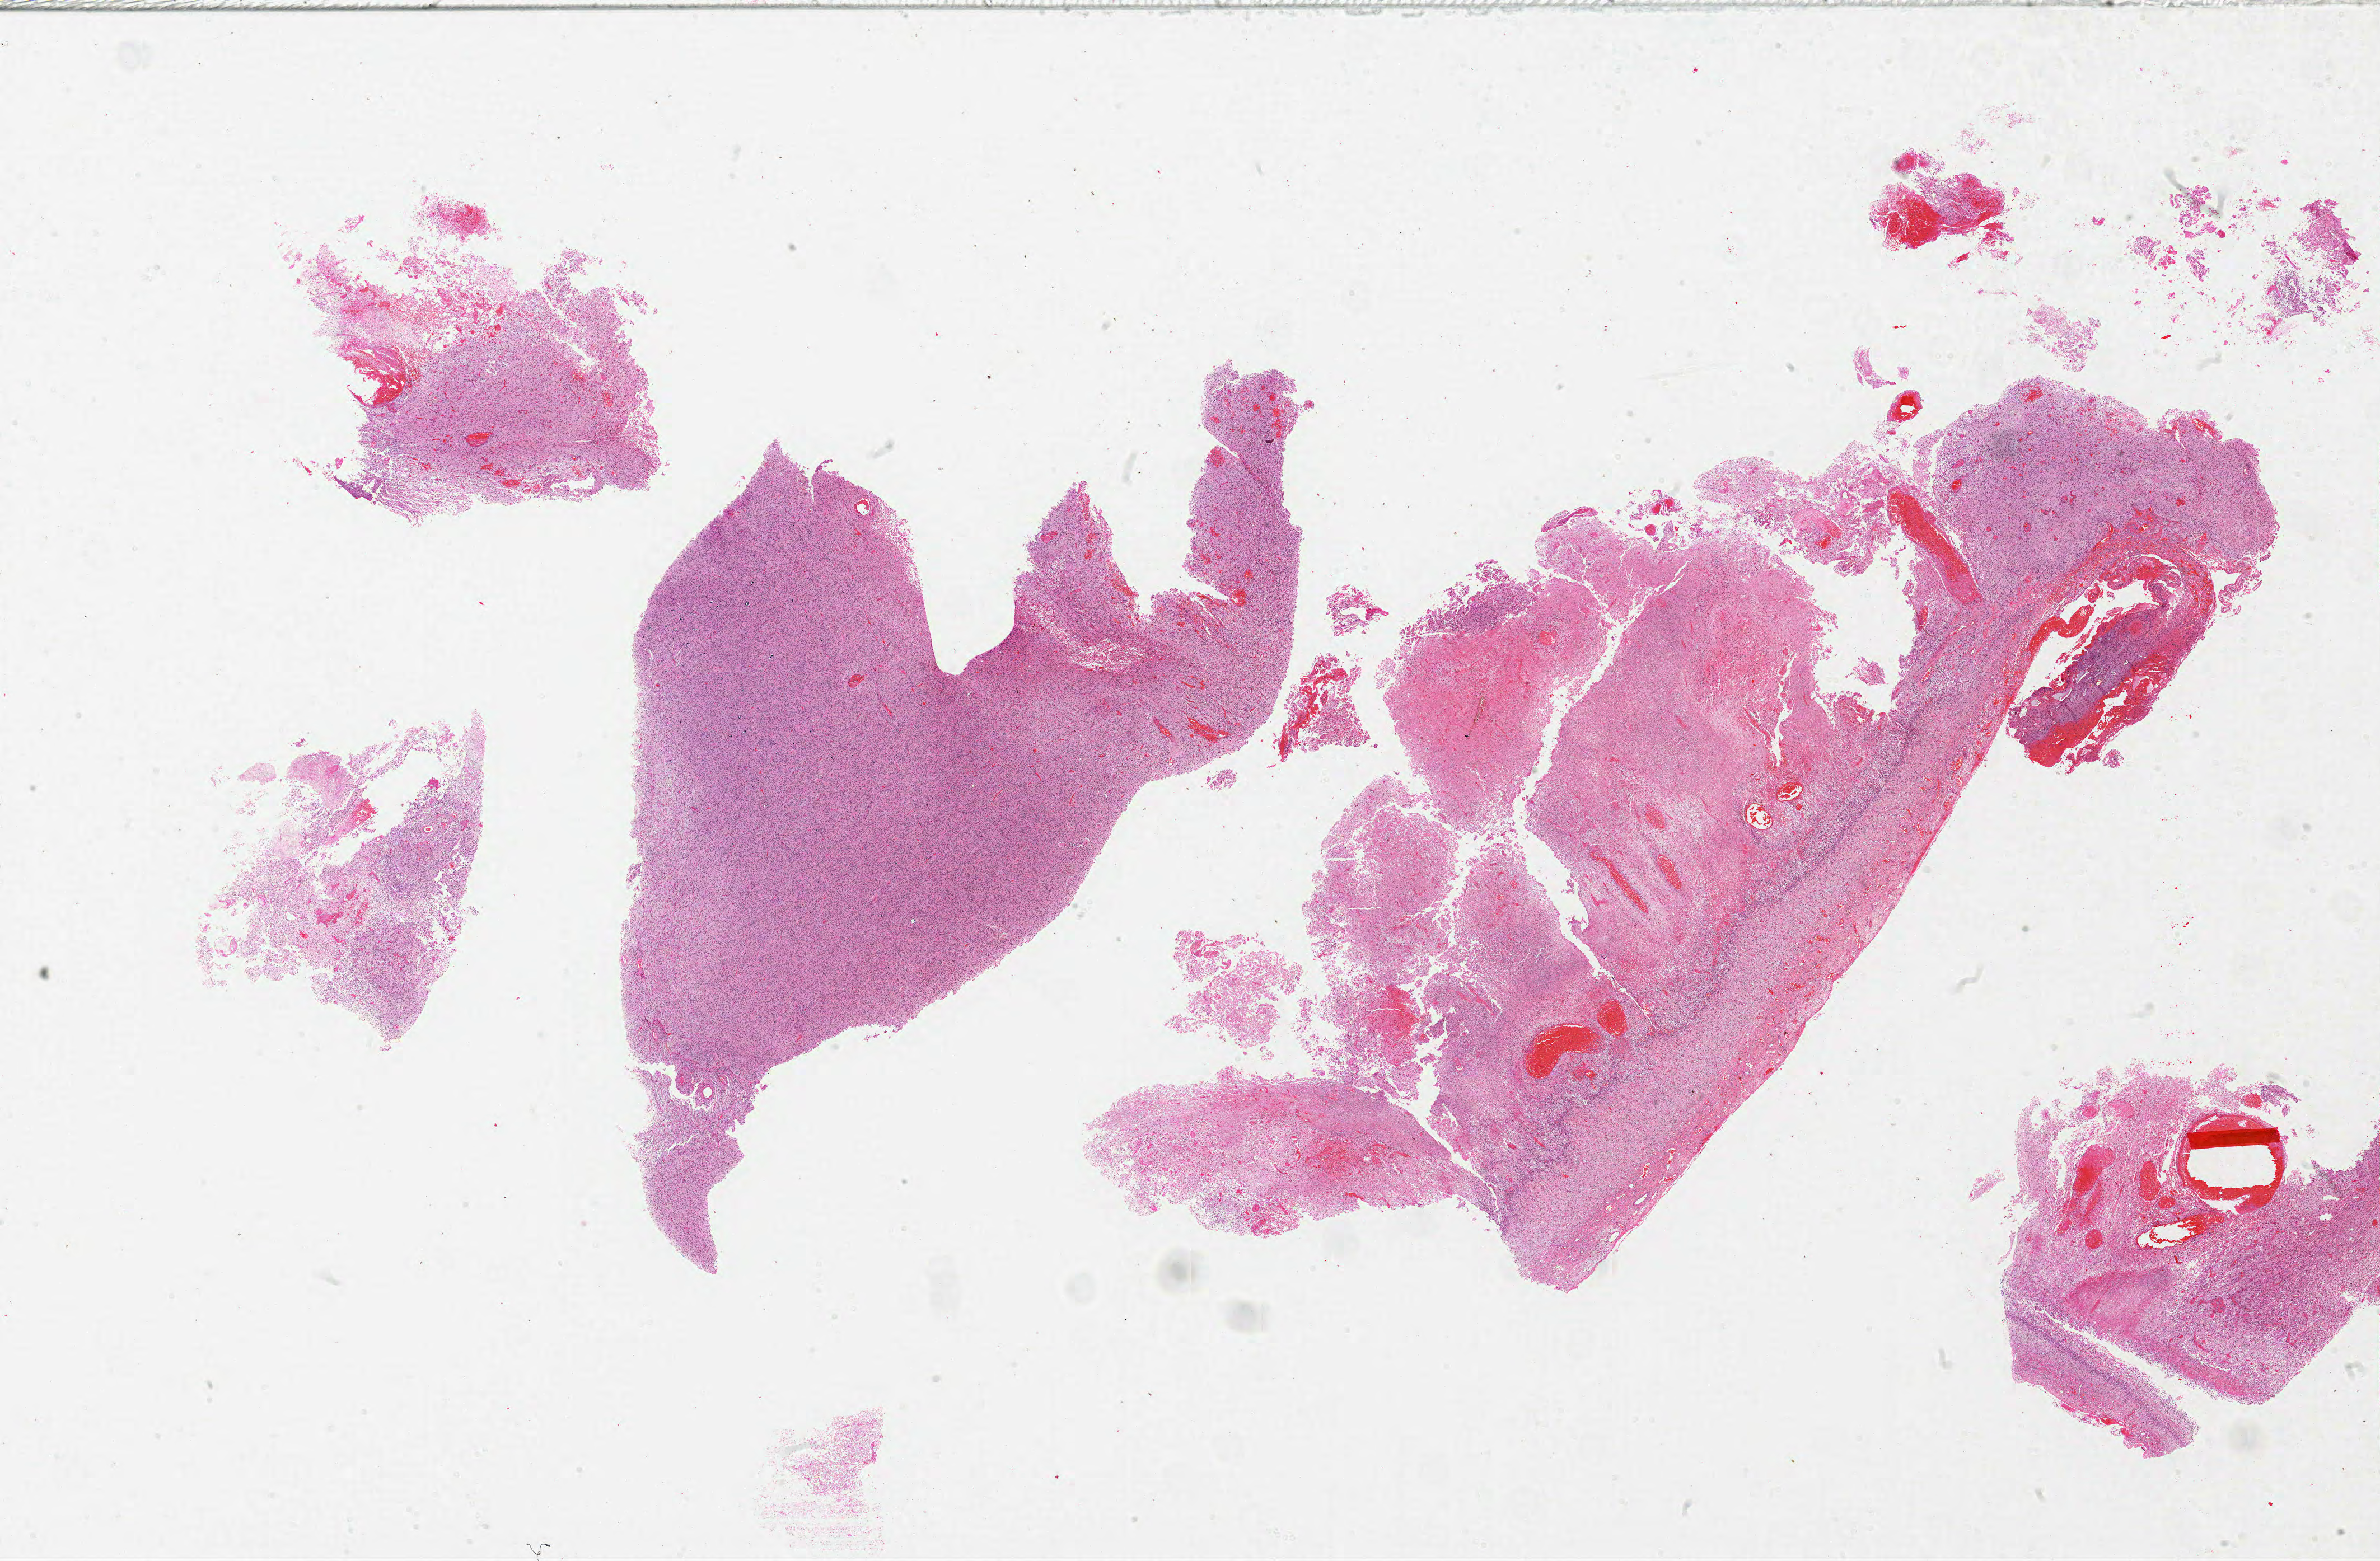
H&E-stained whole-slide image, whole scanned area (about 34.0 x 22.3 mm, slide scanned at 20x) shown as a low-resolution overview; FFPE section; sample: primary tumour, brain. Female, age 48 years at initial diagnosis.
* diagnosis: Glioblastoma